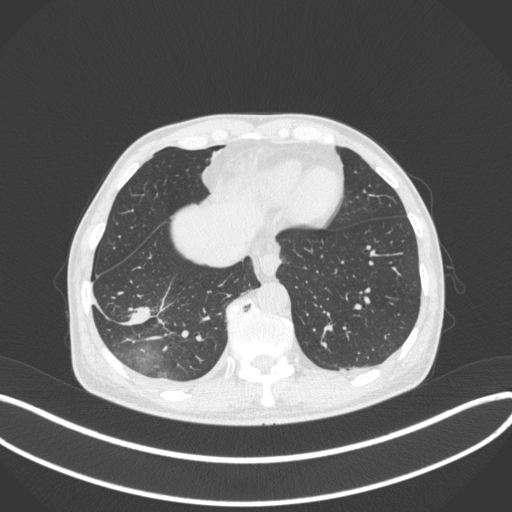
Chest CT, one axial slice. Slice 91 of 385 in the series (ordered by position). 120 kVp. Lung window (W 1500 / L -600 HU). 1 mm slice thickness. 512 × 512 image matrix, field of view 400 × 400 mm. Patient: male, 64 years. Case-level facts recorded for this patient, not image findings: clinical TNM (as recorded): T3 N0 M0; histopathological grade: G2-3.
Structures marked on this image (rectangle marked by the reading radiologist):
- lung tumour (recorded histology: adenocarcinoma): bounding box <120,302,151,333> (left, top, right, bottom; pixels)